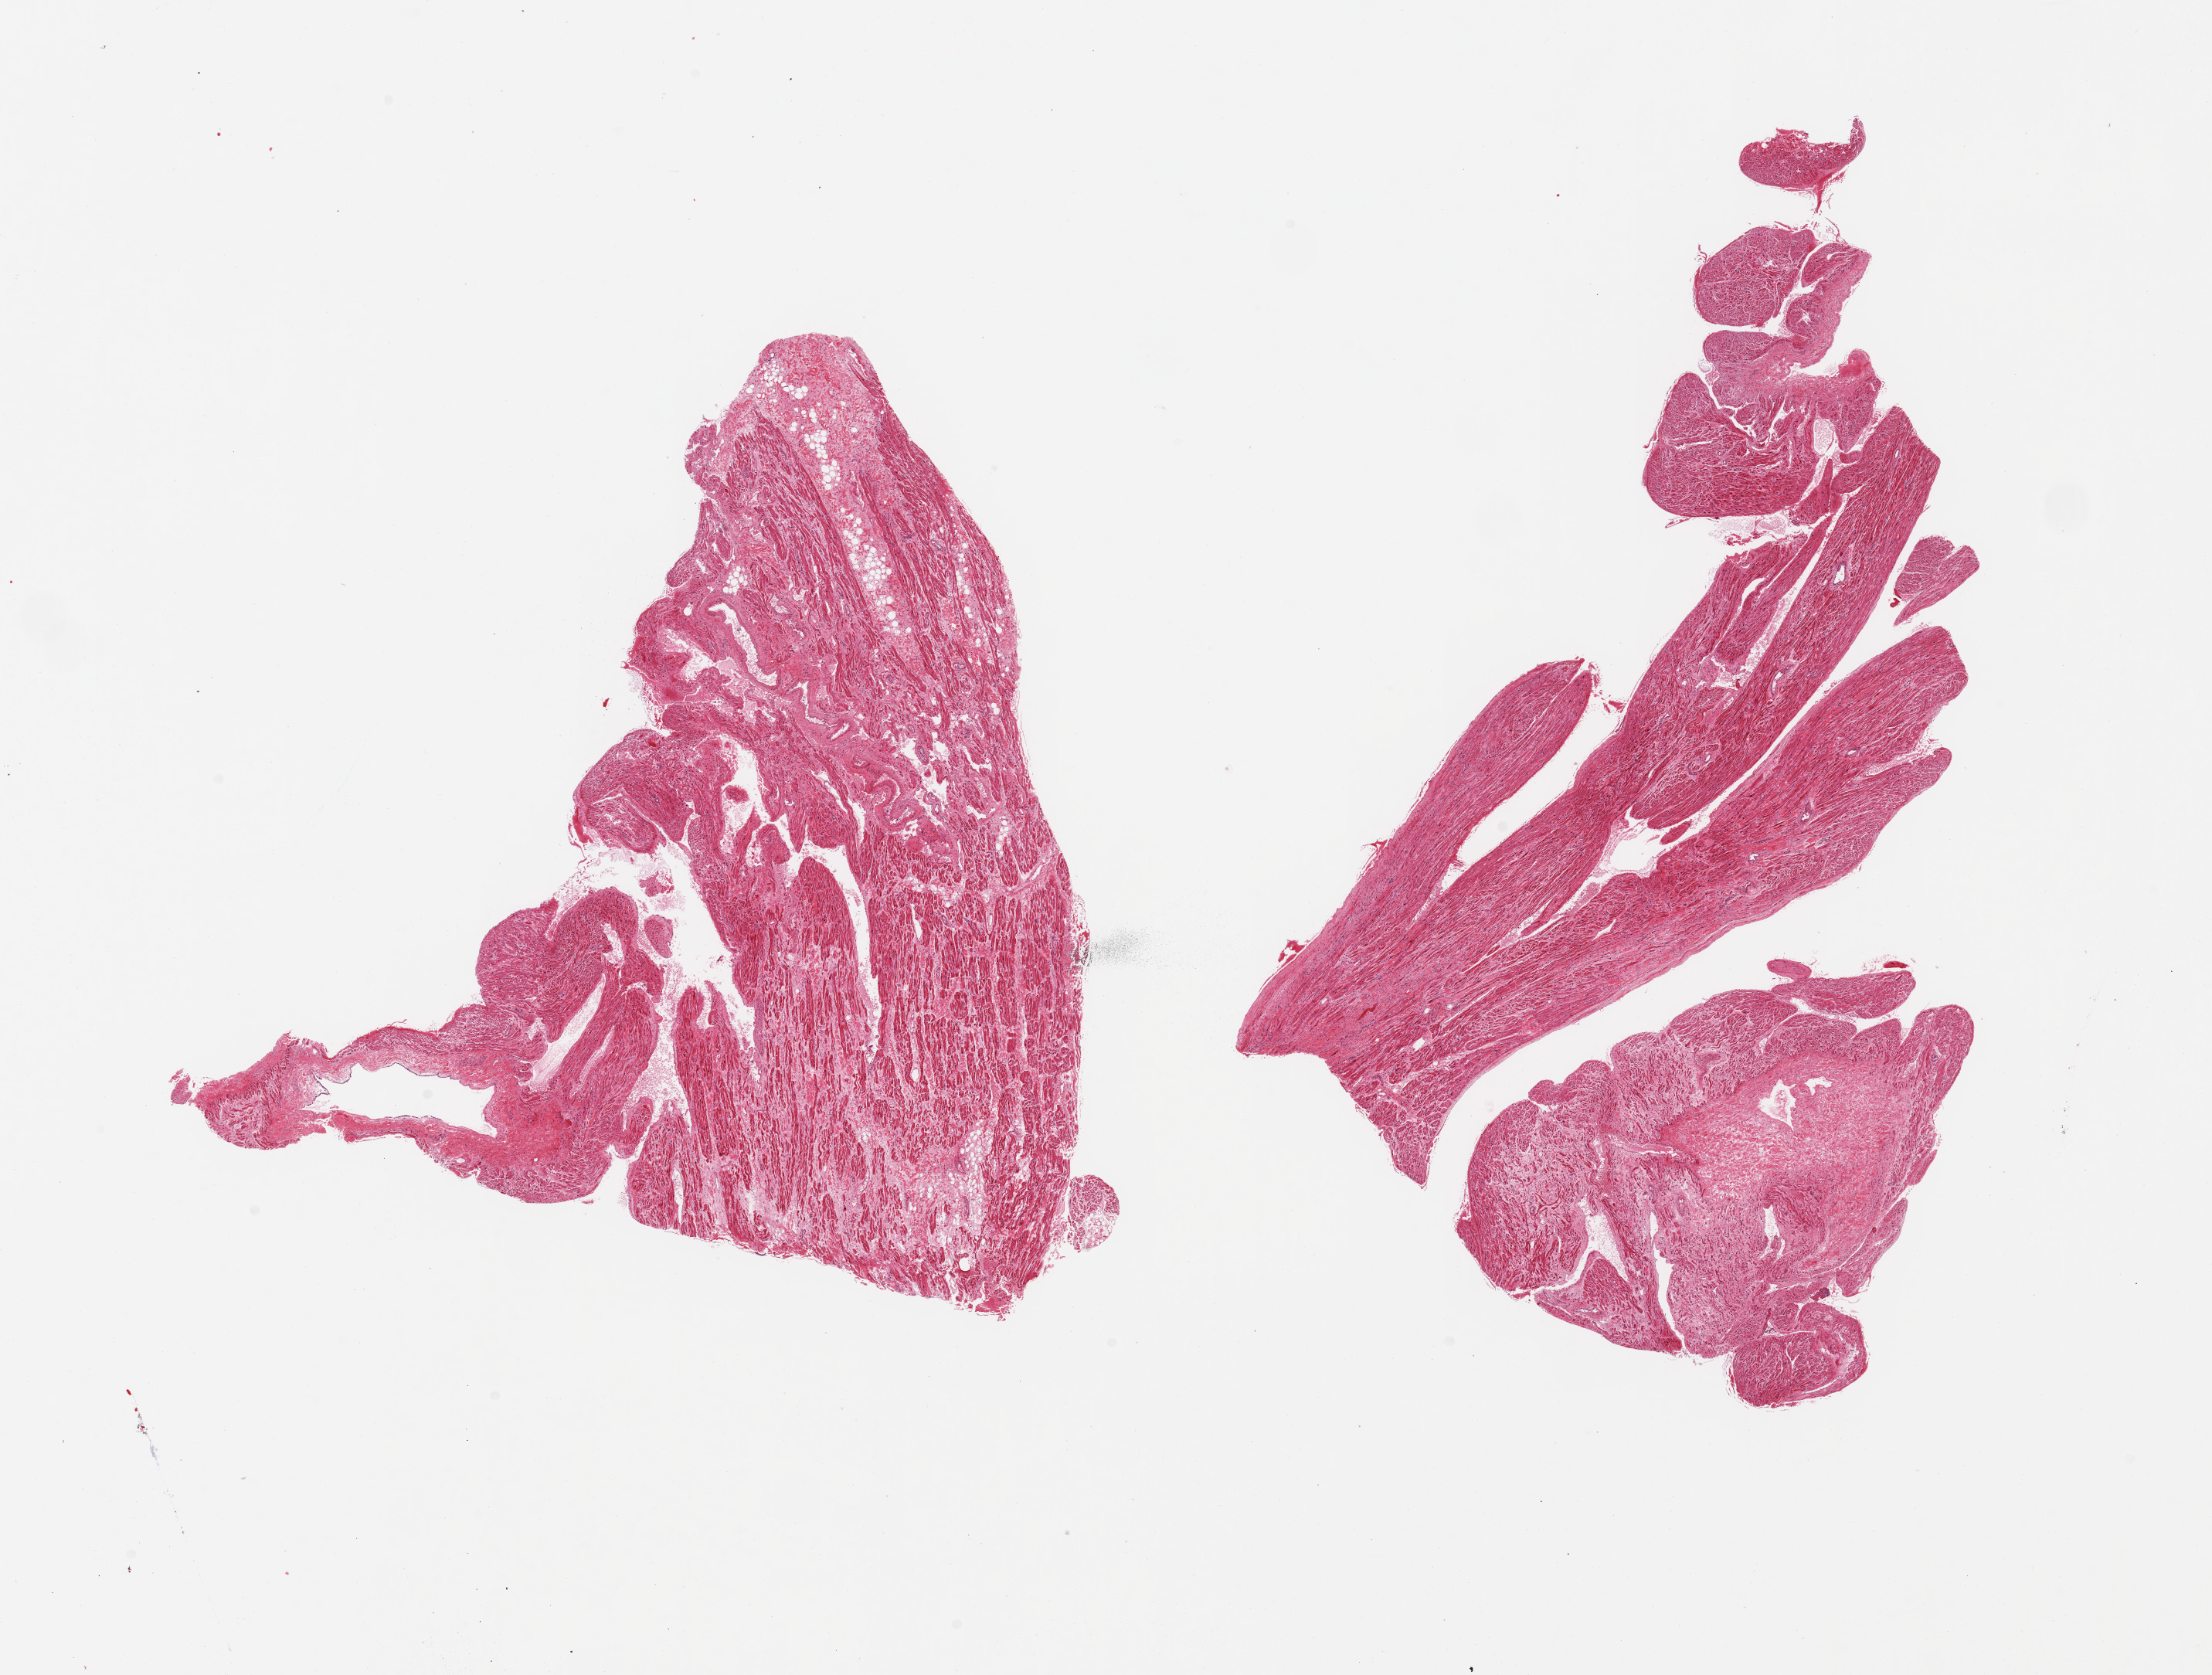
Digitized H&E-stained section, whole scanned area (about 22.6 x 17.1 mm) shown as a low-resolution overview, PAXgene-fixed paraffin-embedded (PFPE) section, sampled site (target tissue): auricular appendage, tissue donor sample. Donor: female.
Pathologist's review note for this sample: 2 pieces; fibrous content up to 20%.